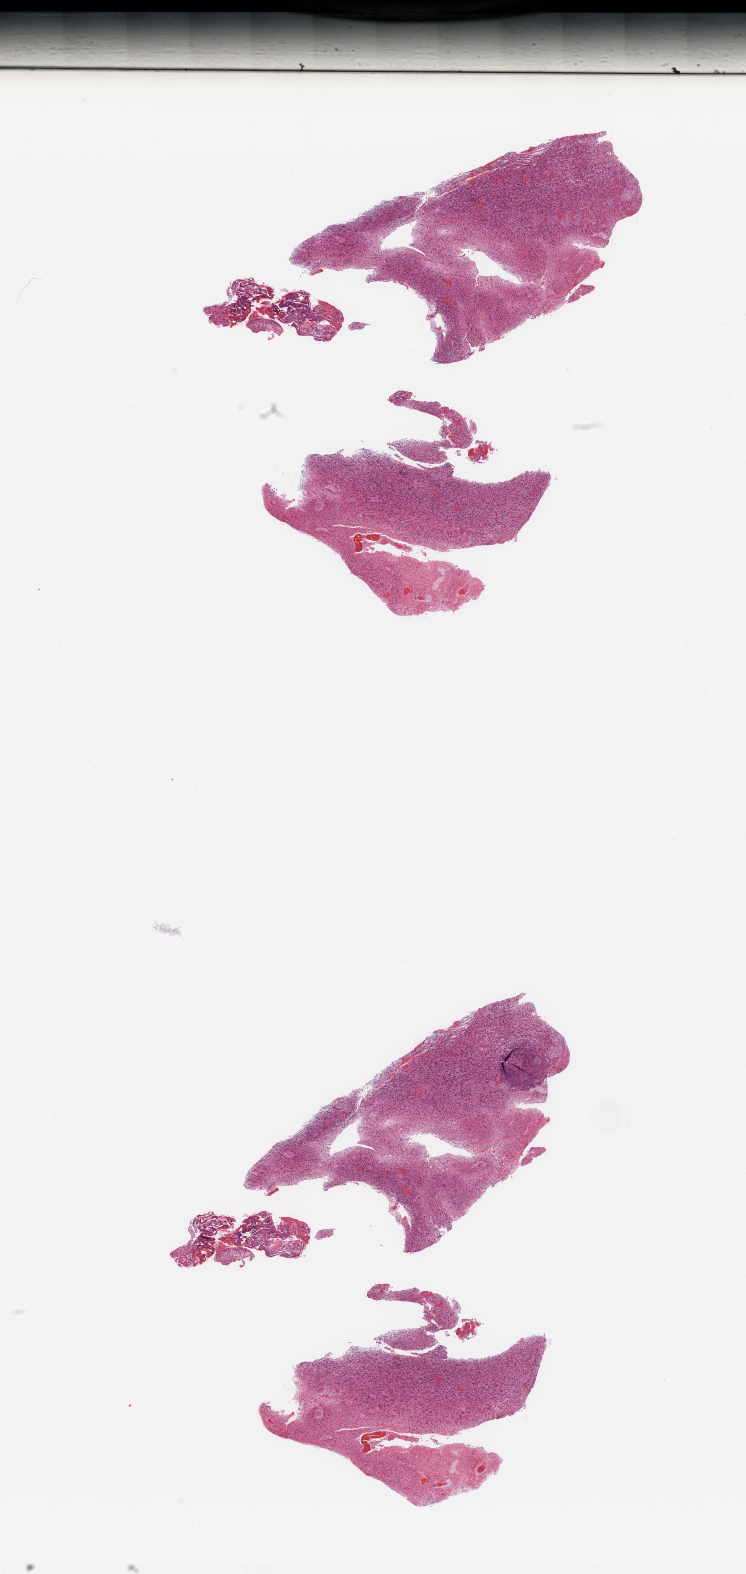
Digitized Hematoxylin and eosin (H&E) stained tissue section (whole slide), whole scanned area (about 11.8 x 24.9 mm) shown as a low-resolution overview. Tumour tissue sample, sampled site: frontal lobe. Male, 58 y/o. Slide review estimates, as recorded: tumour nuclei 80%, necrosis 5%.
• histologic diagnosis: Glioblastoma
• primary tumour site (as recorded): frontal lobe